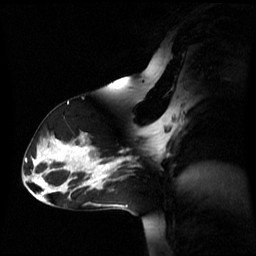
Breast MRI (dynamic contrast-enhanced), one sagittal slice; dynamic contrast-enhanced series, image 2 of 3 at this slice position (ordered by acquisition); 1.5 T; TE 4.2 ms, TR 8.4 ms; 2.6 mm slice thickness; 256 × 256 image matrix, field of view 270 × 270 mm. Female patient, age 39 years. Case-level facts recorded for this patient, not image findings: setting: breast cancer imaged before/during neoadjuvant chemotherapy; receptor status: triple-negative.
Structures marked on this image (semi-automatically segmented with operator editing):
- analysis volume of interest (the breast-tissue region the enhancement analysis was run in; not a lesion): box from (x=105, y=149) to (x=148, y=178) px
- tumour enhancement mask (voxels above the 70 % enhancement threshold inside the analysis volume of interest): (x=105, y=159)–(x=124, y=177)